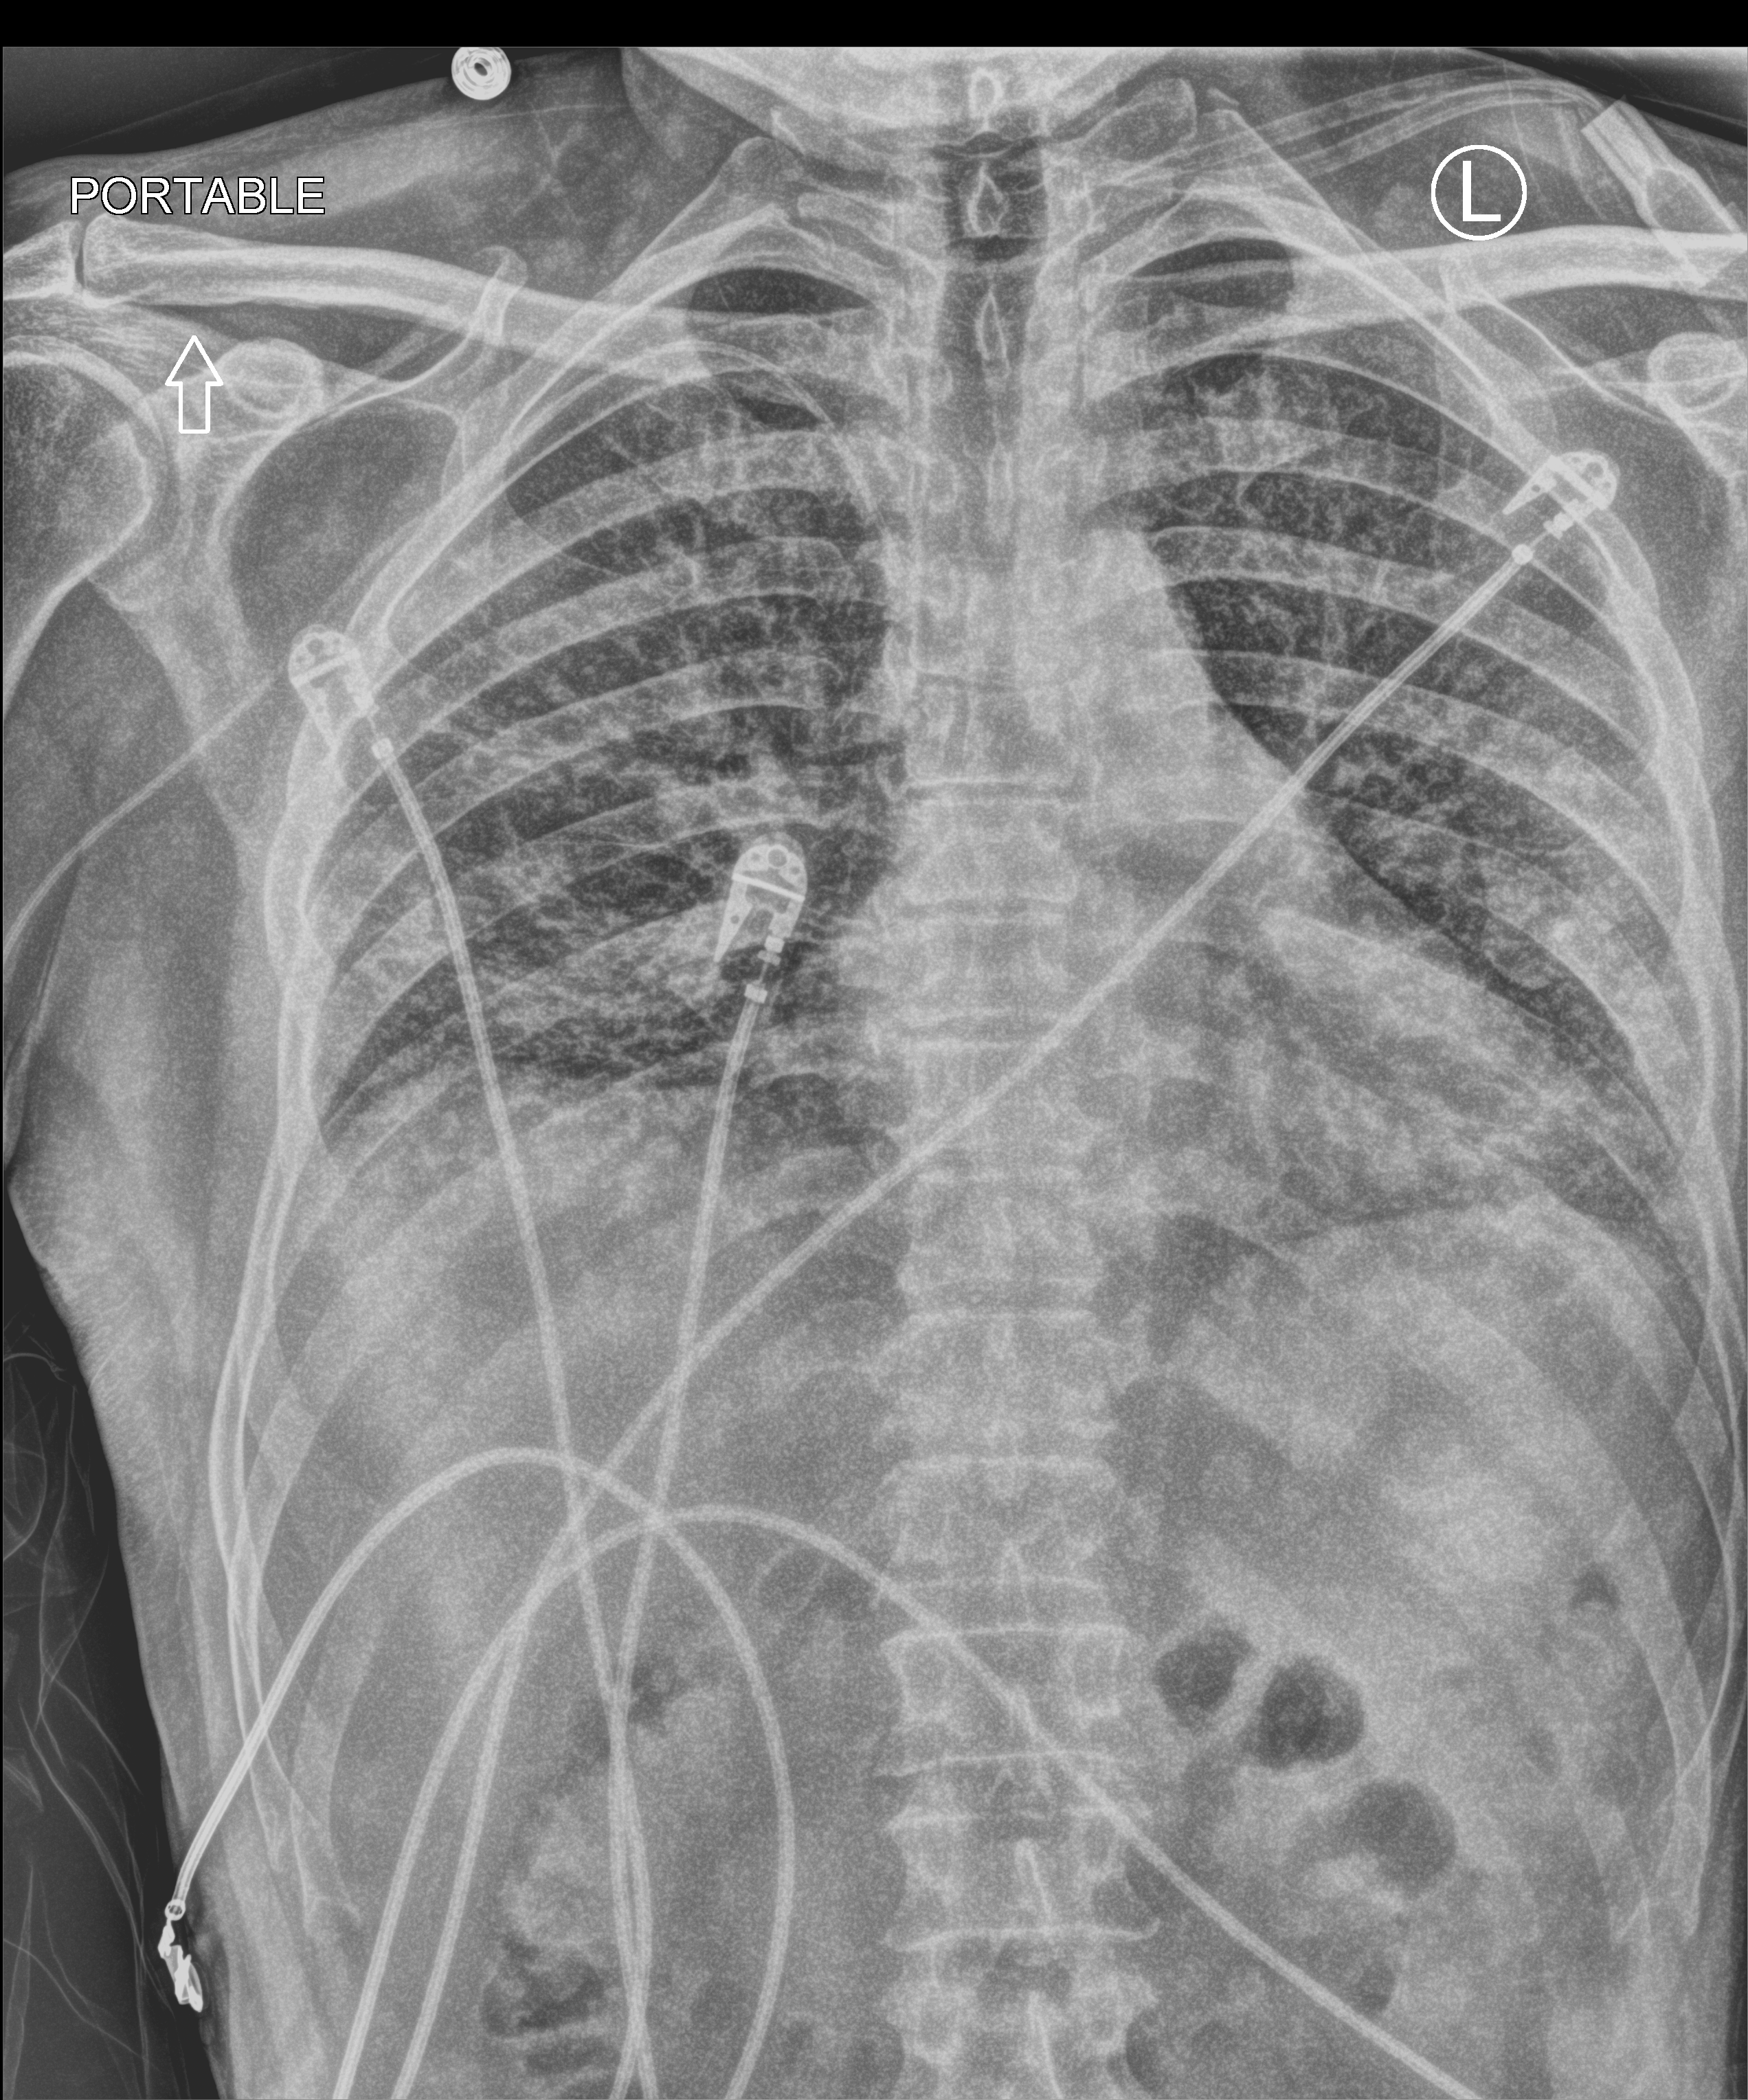
Portable chest radiograph; anteroposterior (AP) projection. Male patient hospitalised with COVID-19, age 18–59 years.
Hospital-stay facts (about this admission, not read from this image; timing relative to this image not recorded): mechanically ventilated during this hospital stay: no; chronic kidney disease (admission record): no; admitted to intensive care during this hospital stay: yes.